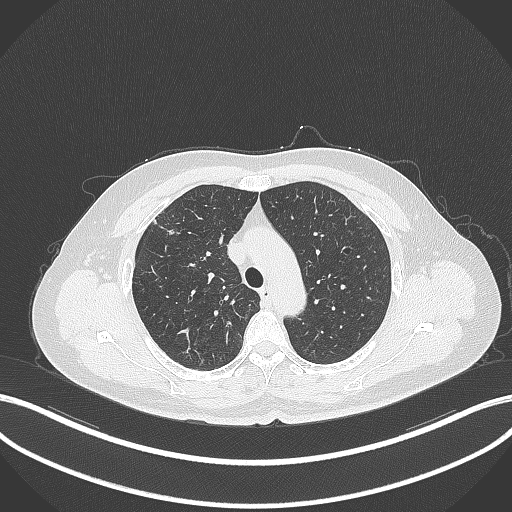
Chest CT, one axial slice; slice 269 of 353 in the series (ordered by position); reconstruction kernel B70f; 120 kVp; lung window (W 1500 / L -600 HU); 1 mm slice thickness; 512 × 512 image matrix, field of view 400 × 400 mm. Patient: female, 56 years. From the clinical record (not read from this slice): clinical TNM (as recorded): T1c N0 M0.
Outlined on this slice (bounding box drawn by a radiologist):
- lung tumour (recorded histology: adenocarcinoma): box from (x=165, y=224) to (x=175, y=236) px